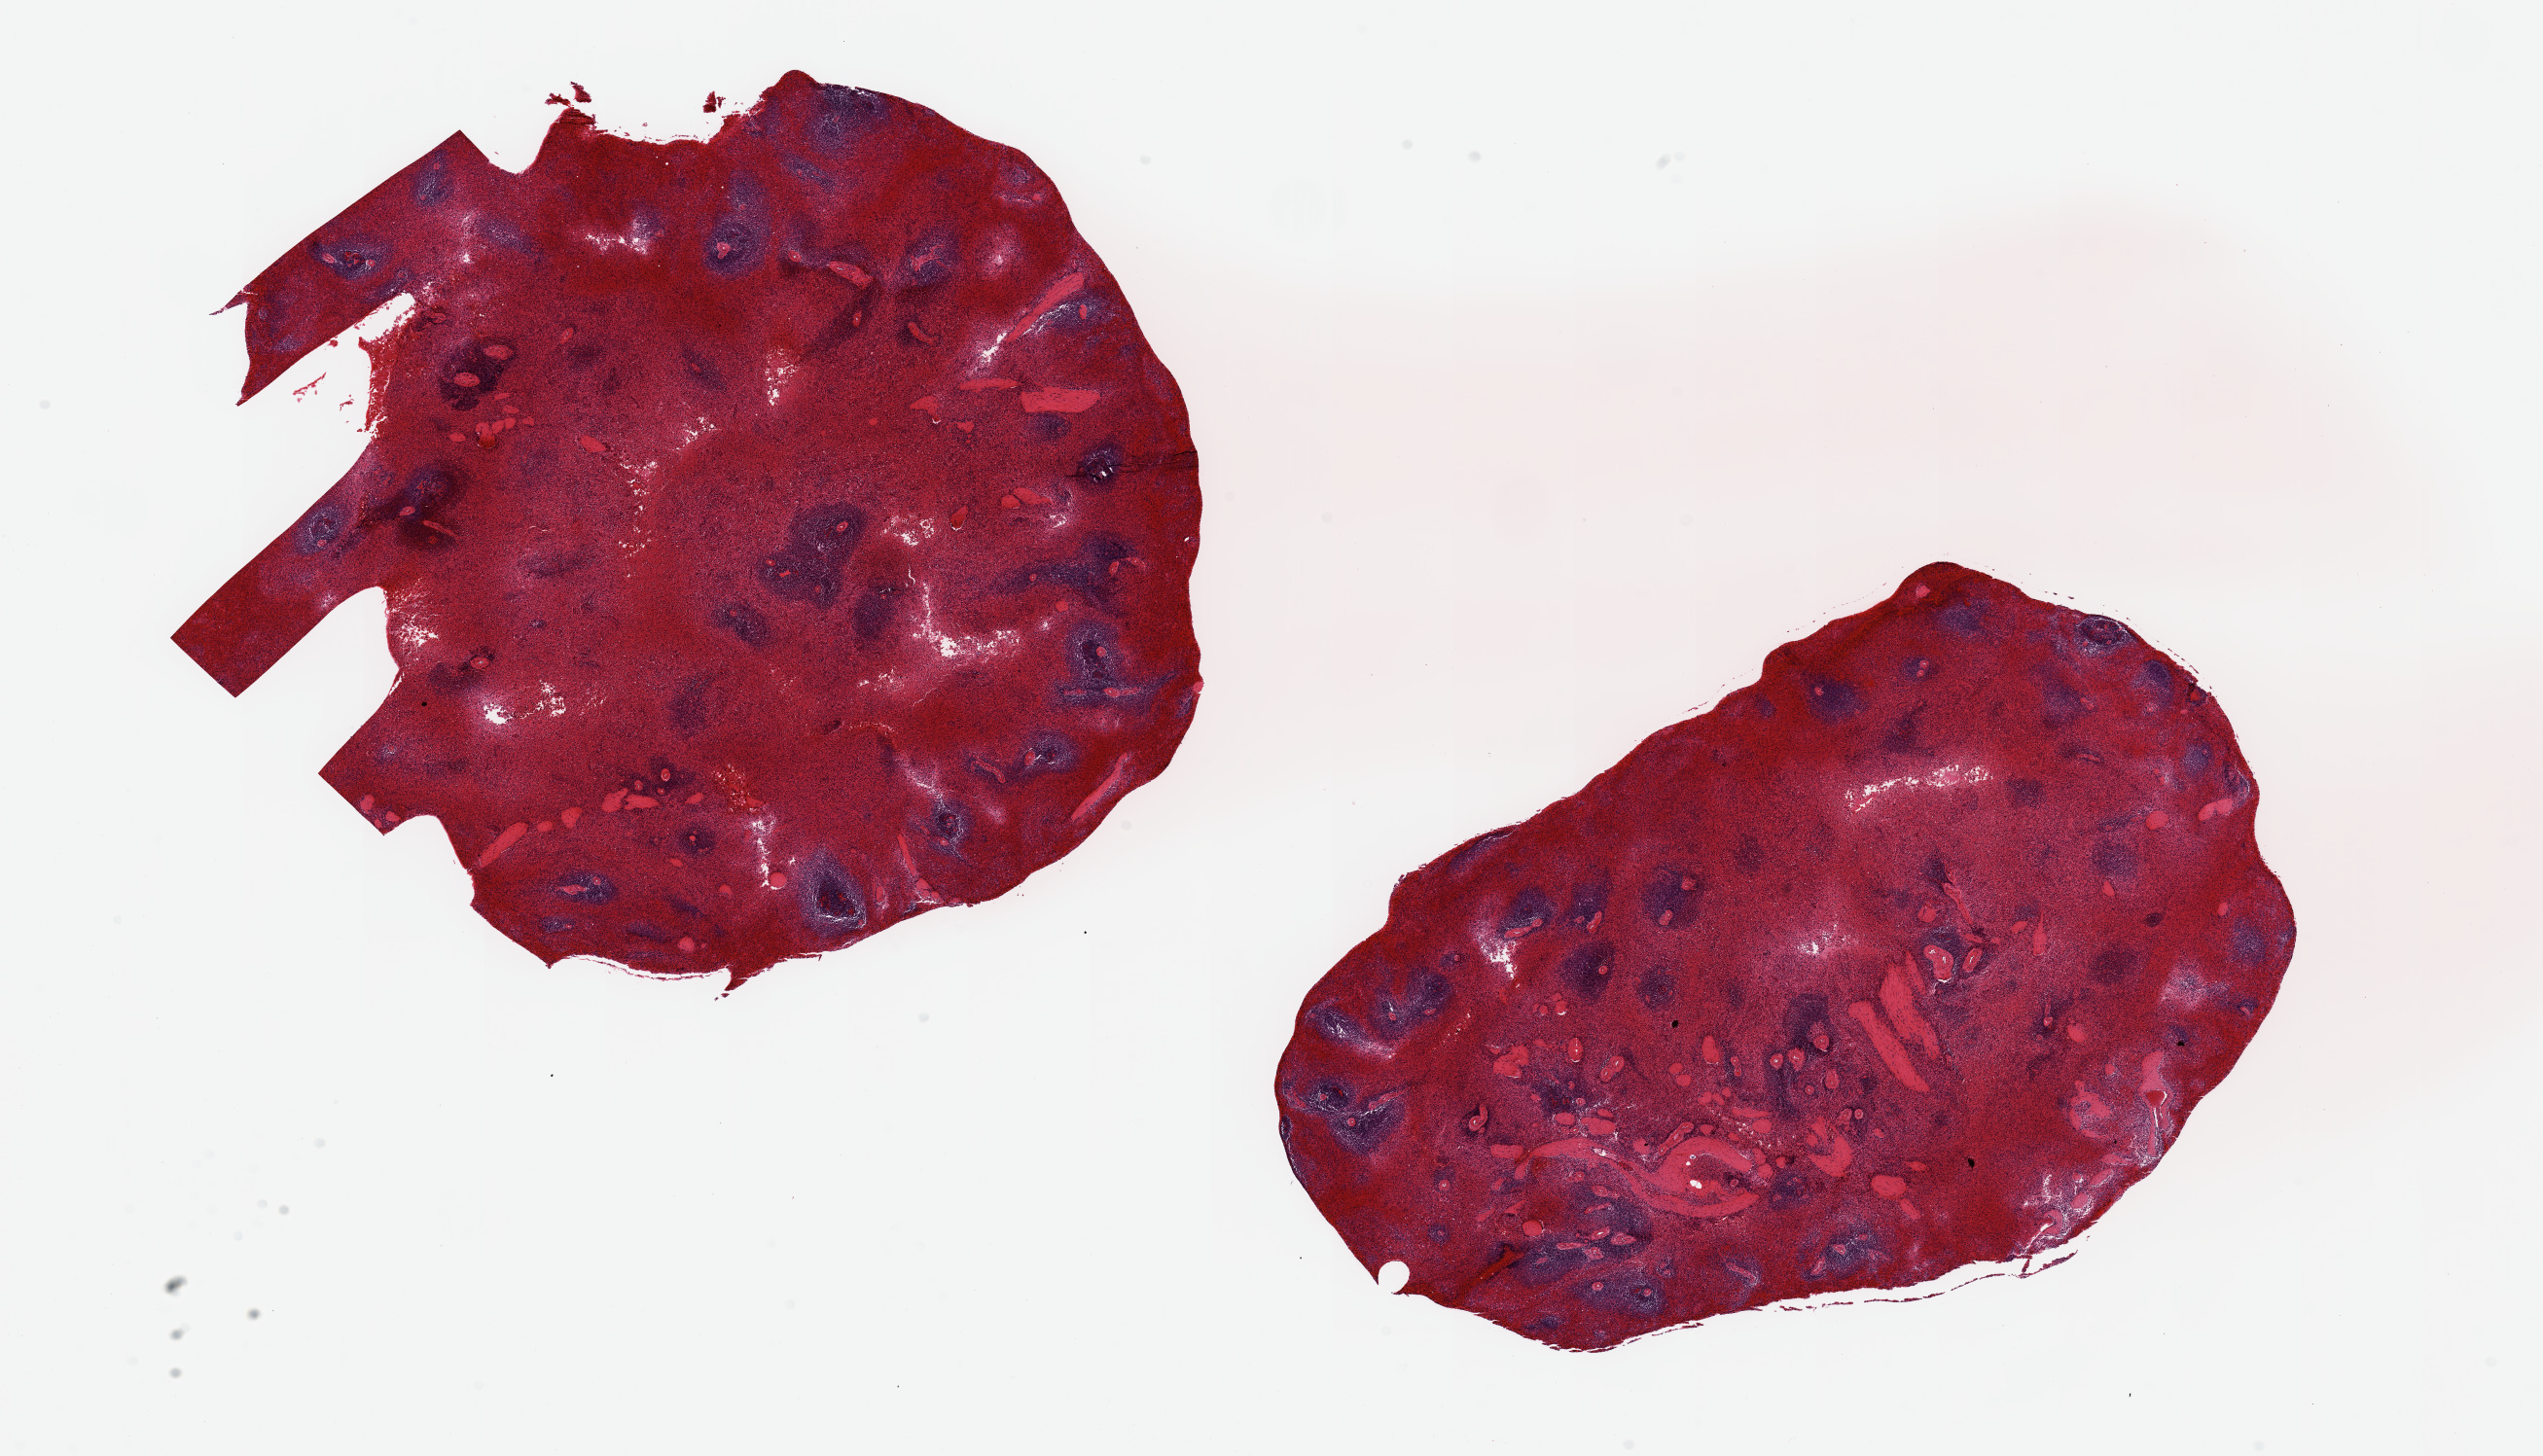
Digitized haematoxylin and eosin-stained section, low-resolution overview of the scanned area, about 20.7 x 11.8 mm; PAXgene-fixed paraffin-embedded (PFPE) section; target tissue: spleen; tissue donor sample. Donor: male.
- reviewer comment on this tissue sample: 2 pieces 7x7 & 7x4 mm; moderately congested red pulp; large piece shows cassette grid compression artifact